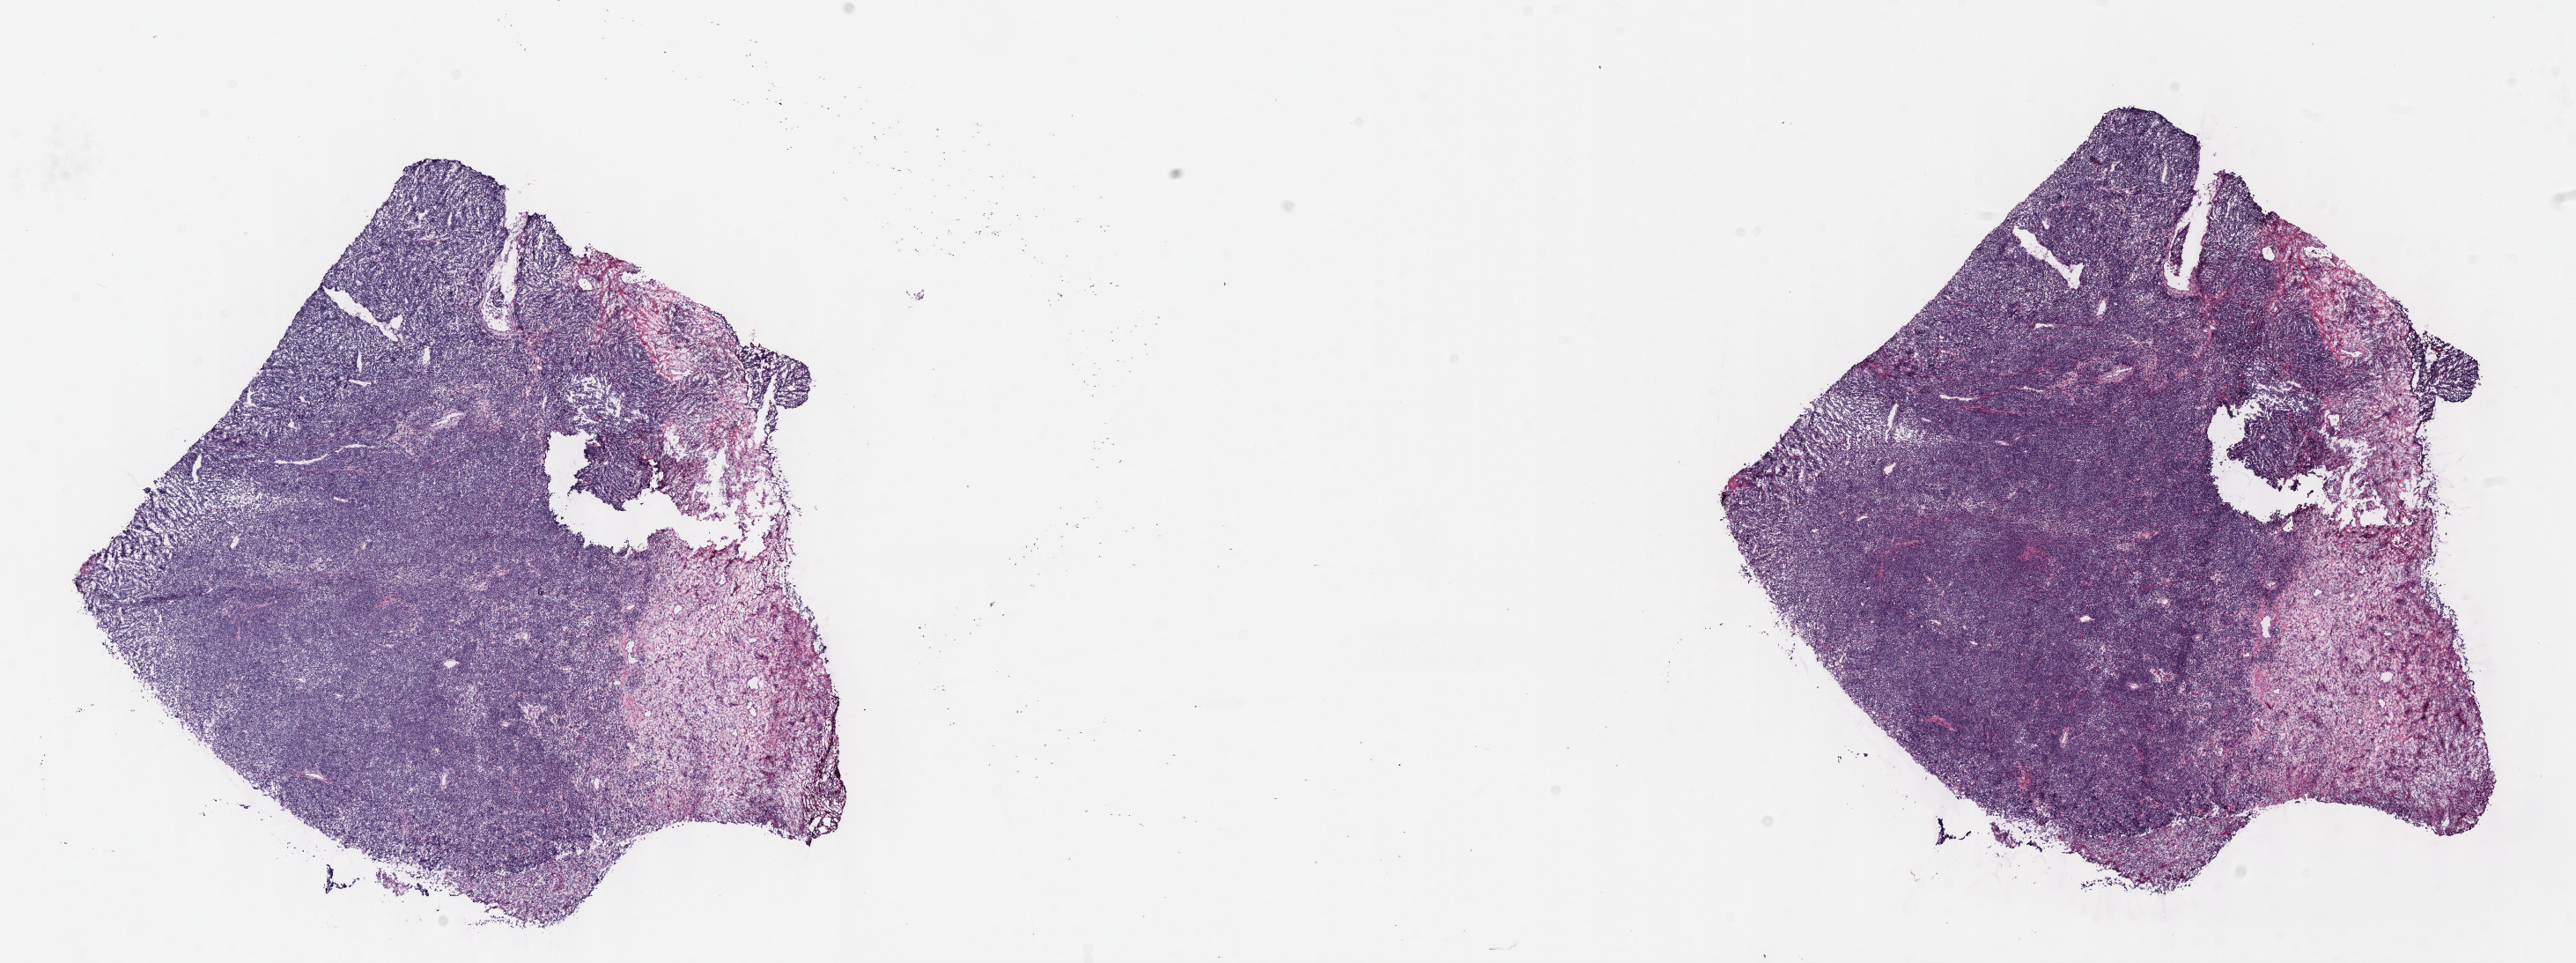
Digitized H&E-stained section — a low-resolution overview of the entire scanned area, about 23.6 x 8.8 mm, frozen section, specimen: primary tumor, site: cranium. Patient: female, aged 11. Composition of this section per pathologist review: tumor cells 80%, tumor nuclei 90%, stromal cells 20%, necrosis 0%, normal cells 0%. Infiltration values recorded for this section: lymphocyte infiltration 10%, monocyte infiltration 20%, neutrophil infiltration 10%.
* Ann Arbor stage (patient): Stage I
* section: bottom of the tissue portion
* diagnosis: Burkitt lymphoma, NOS